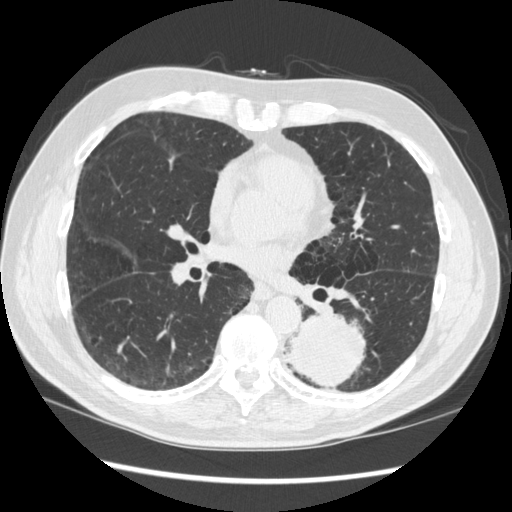
Axial slice from a low-dose chest CT screening exam. Baseline annual screen. Lung window (W 1500 / L -600 HU). 1.25 mm slice thickness. Male, age 72 years at enrolment. Current smoker at enrolment.
Expert reader's lesion annotation, bounding box (x1, y1, x2, y2) in pixels: (267, 303, 371, 395). The screening reader recorded 2 non-calcified nodules or masses ≥4 mm on this exam (left lower lobe, right middle lobe); which of them this box marks is not recorded.